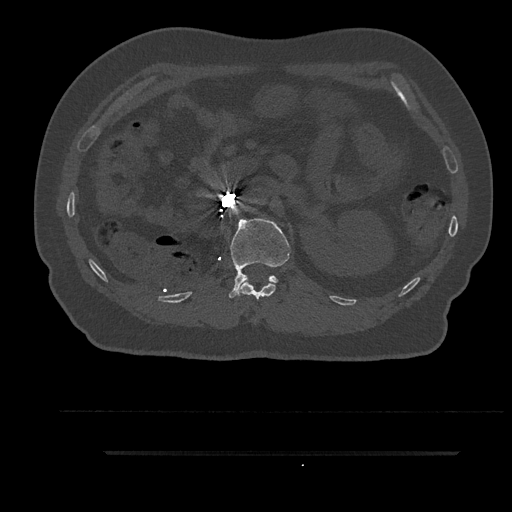
CT including the spine, one axial slice; slice 200 of 797 in the series (ordered by position); 120 kVp; bone window (W 1800 / L 400 HU); 0.5 mm slice thickness; 512 × 512 image matrix, field of view 432 × 432 mm. Male patient, age 63 years. From the clinical record (not read from this slice): primary cancer: renal.
Structures marked on this image (semi-automatic segmentation, software-assisted and operator-edited):
- L1 vertebra: bounding box (x1, y1, x2, y2) in pixels: (229, 218, 291, 298)
- T12 vertebra: (239, 281, 276, 300)